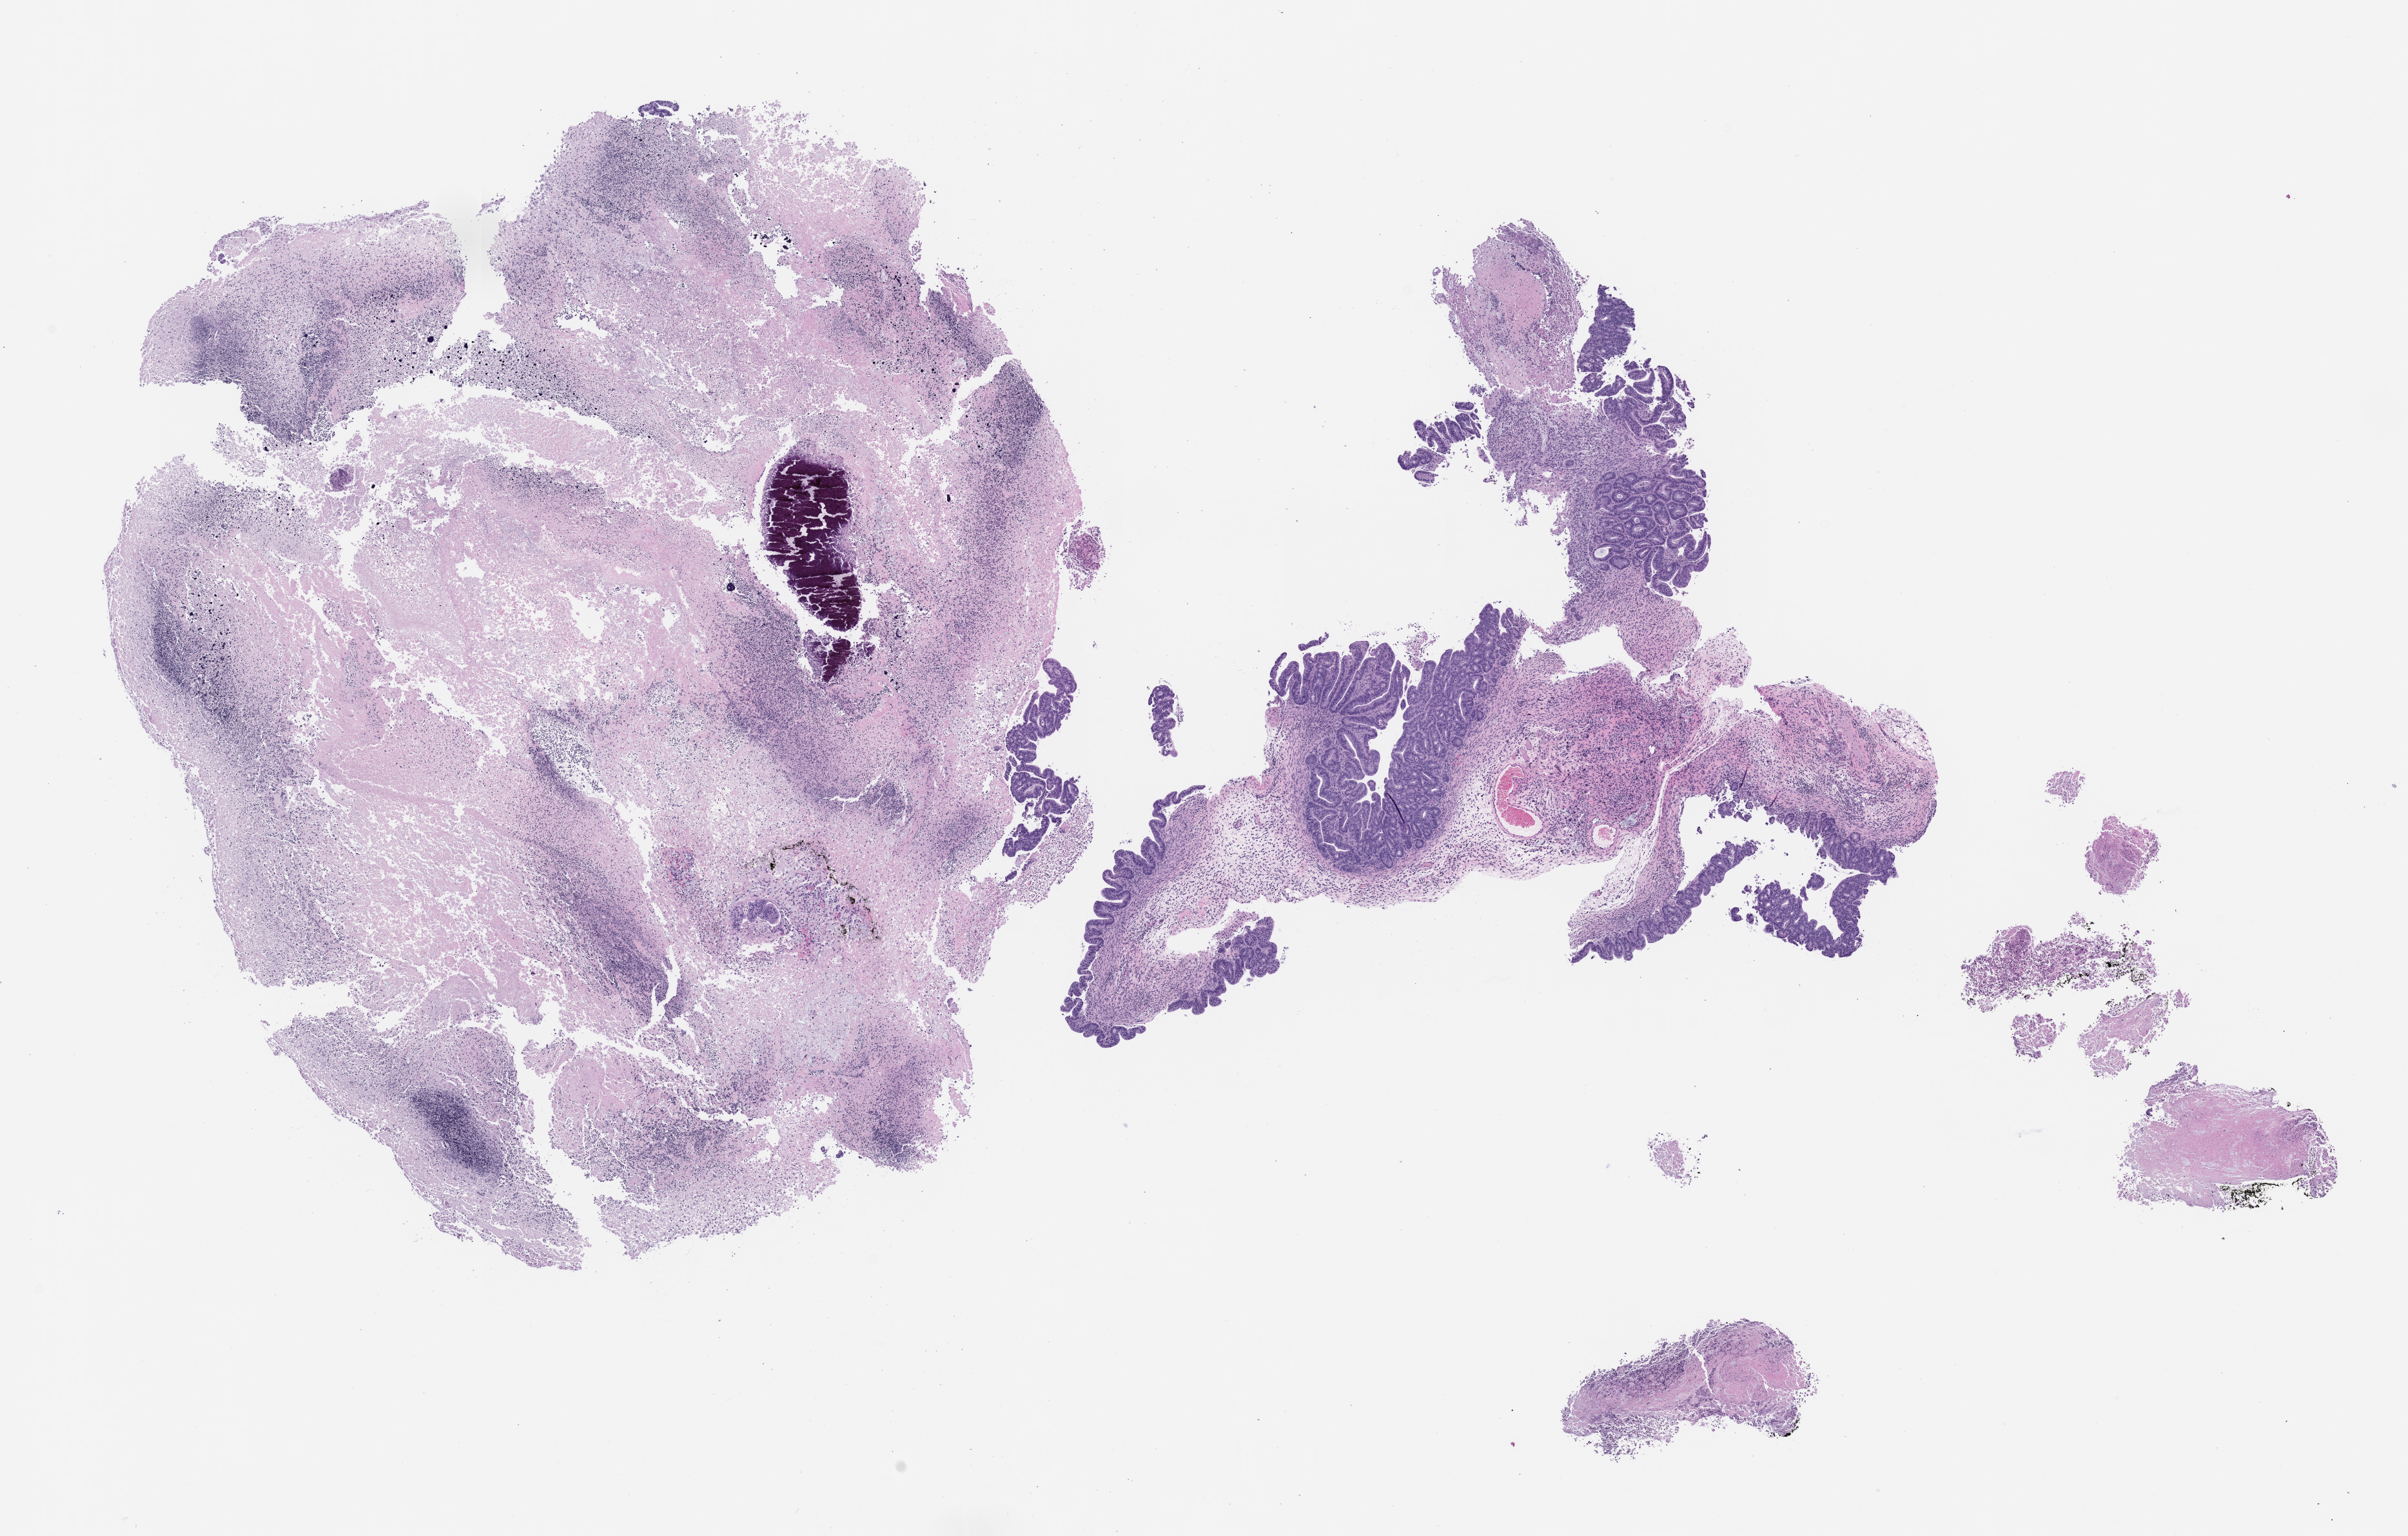
H&E whole-slide image of a patient-derived xenograft (PDX) tumor grown in a mouse, passage 0 — a low-resolution overview of the entire scanned area, about 15.0 x 9.6 mm, FFPE section, originating tumor site category: rectum.
Originating patient diagnosis: Rectal Adenocarcinoma.